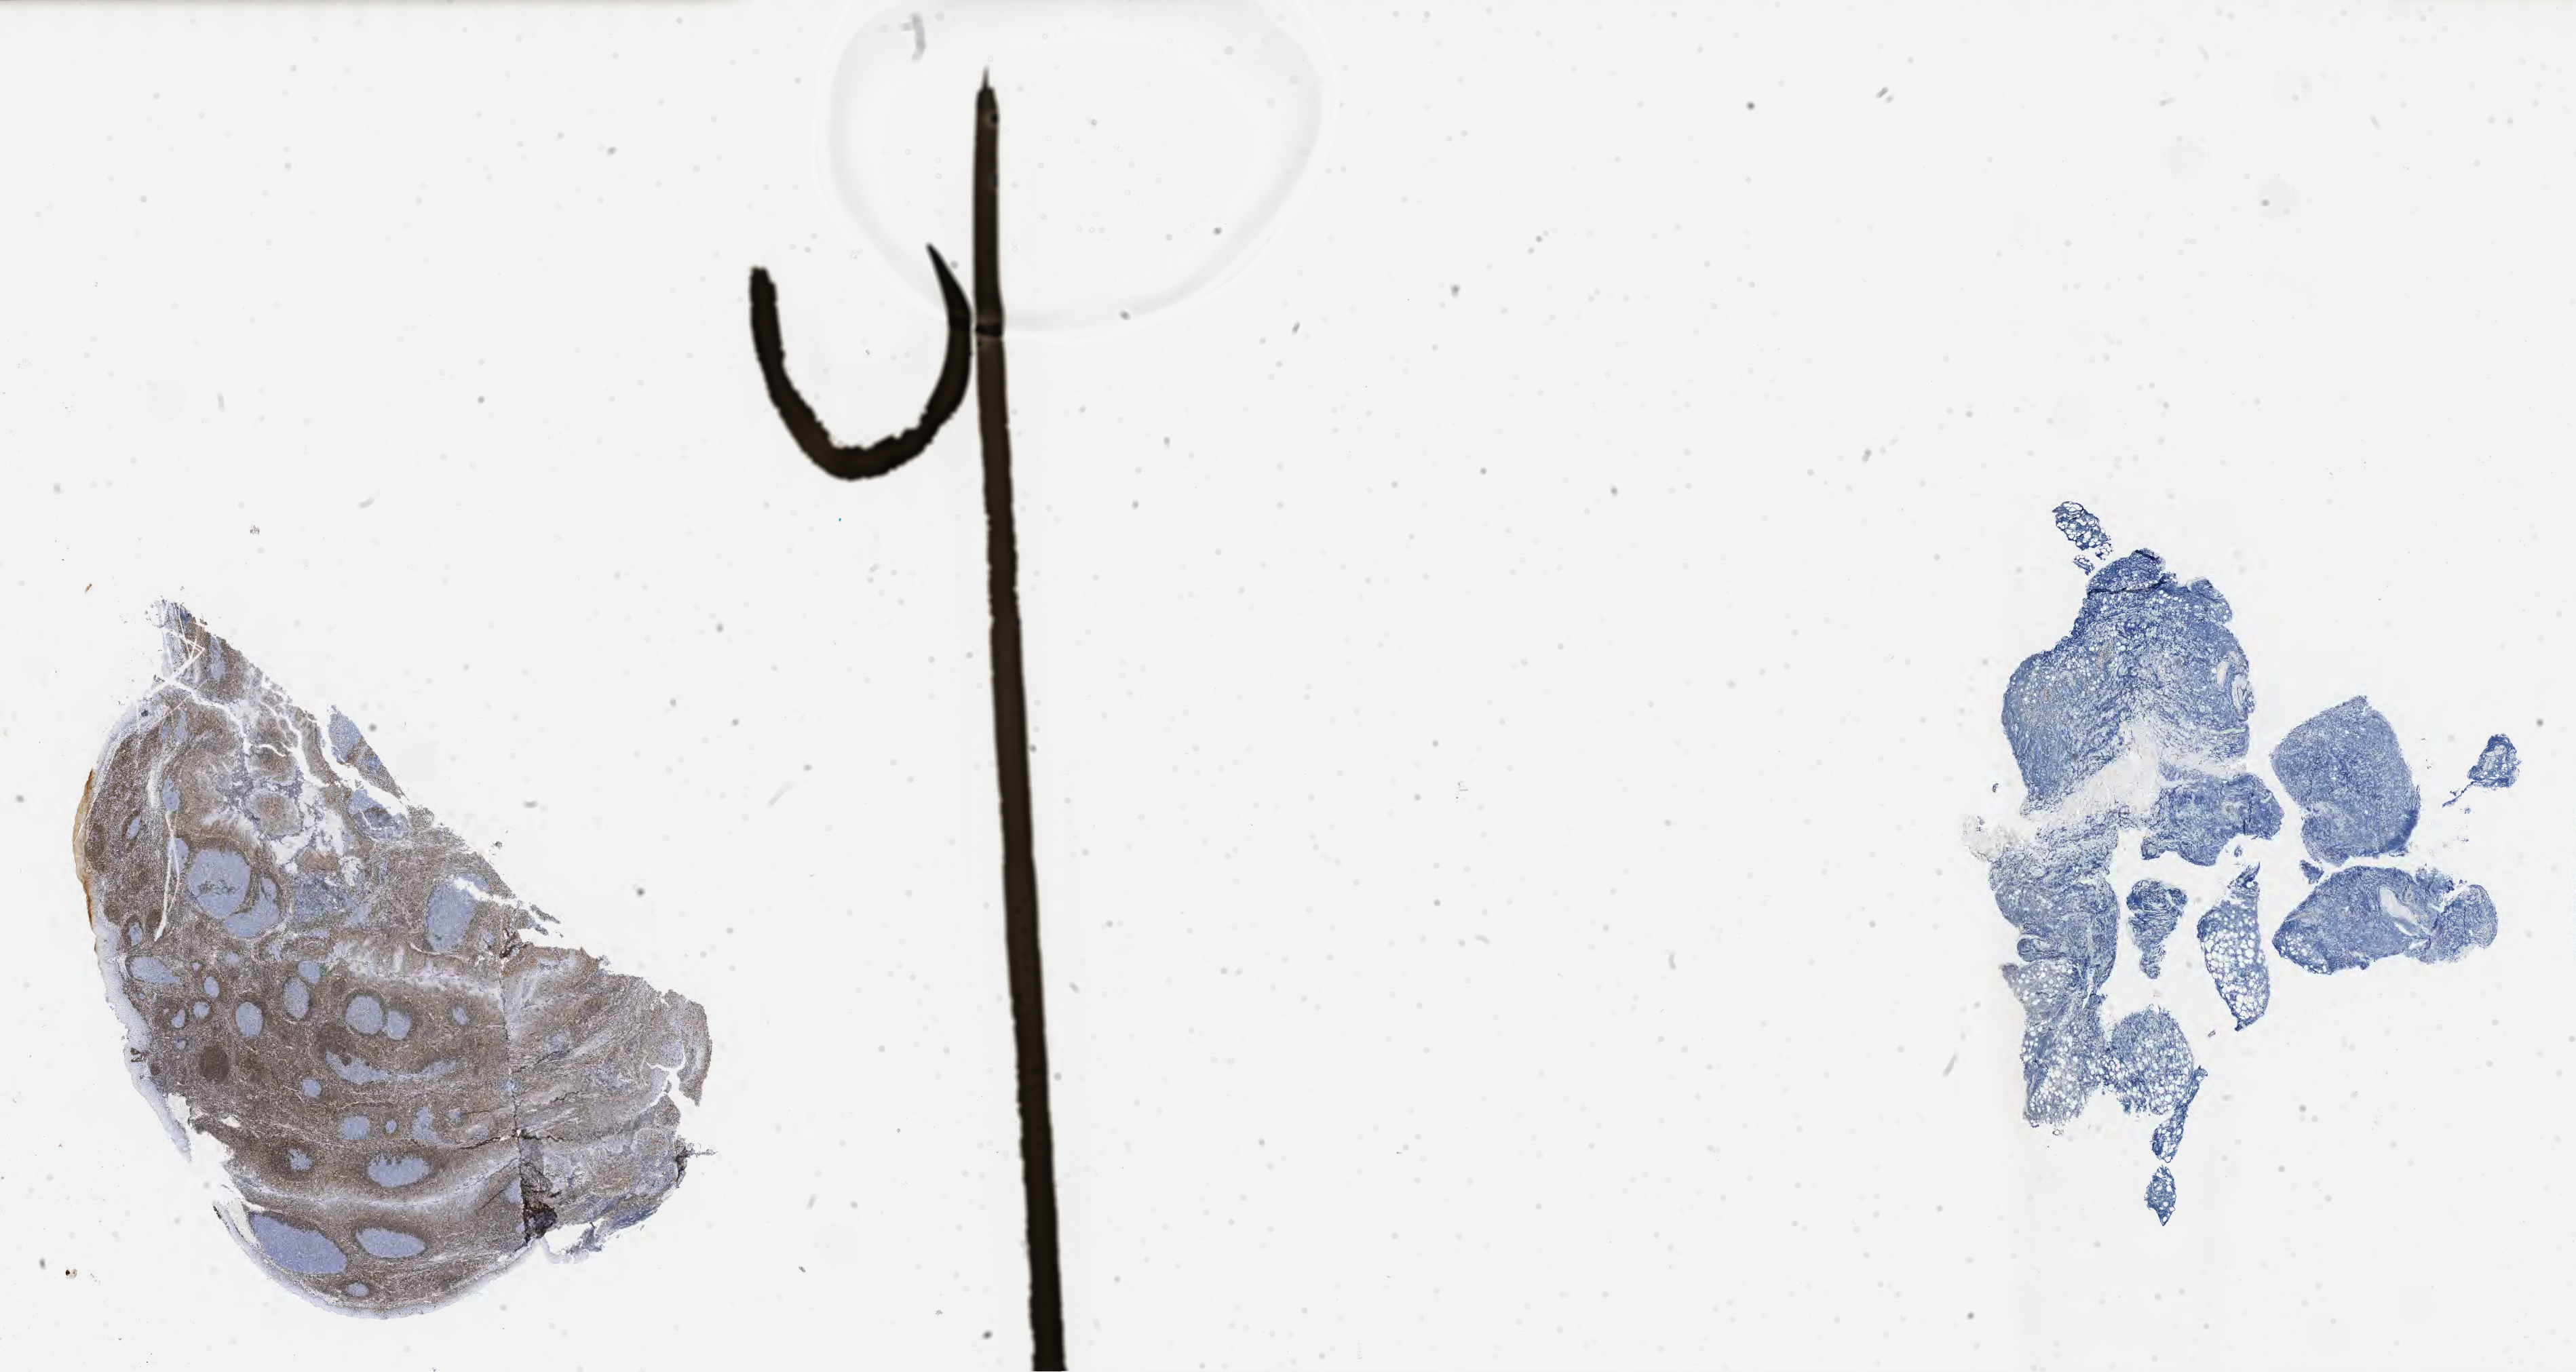
Immunohistochemistry (IHC) whole-slide image stained for BCL2 — whole scanned area (about 30.7 x 16.4 mm) shown as a low-resolution overview; tumor tissue; anatomic site: orbit. Patient: male, 20 years old.
Histologic diagnosis: Burkitt lymphoma, NOS.